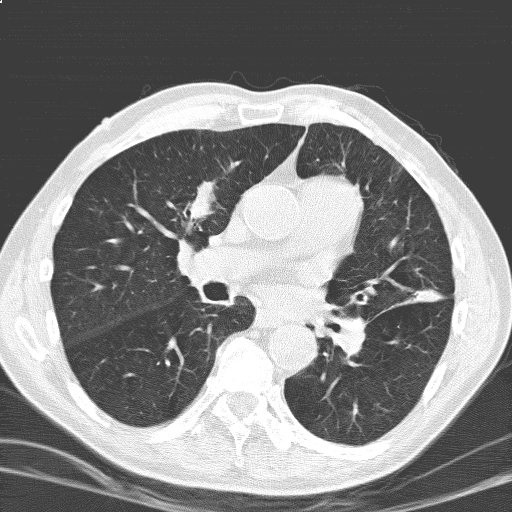
Low-dose screening chest CT, one axial slice. Position 100 of 184 along the scan axis. 120 kVp. Lung window (W 1500 / L -600 HU). 3.2 mm slice thickness. 512 × 512 image matrix, field of view 329 × 329 mm.
Structures marked on this image (expert manual segmentation):
- lesion 1 (tumor, upper lobe of right lung): bounding box (x1, y1, x2, y2) in pixels: (187, 182, 215, 222)